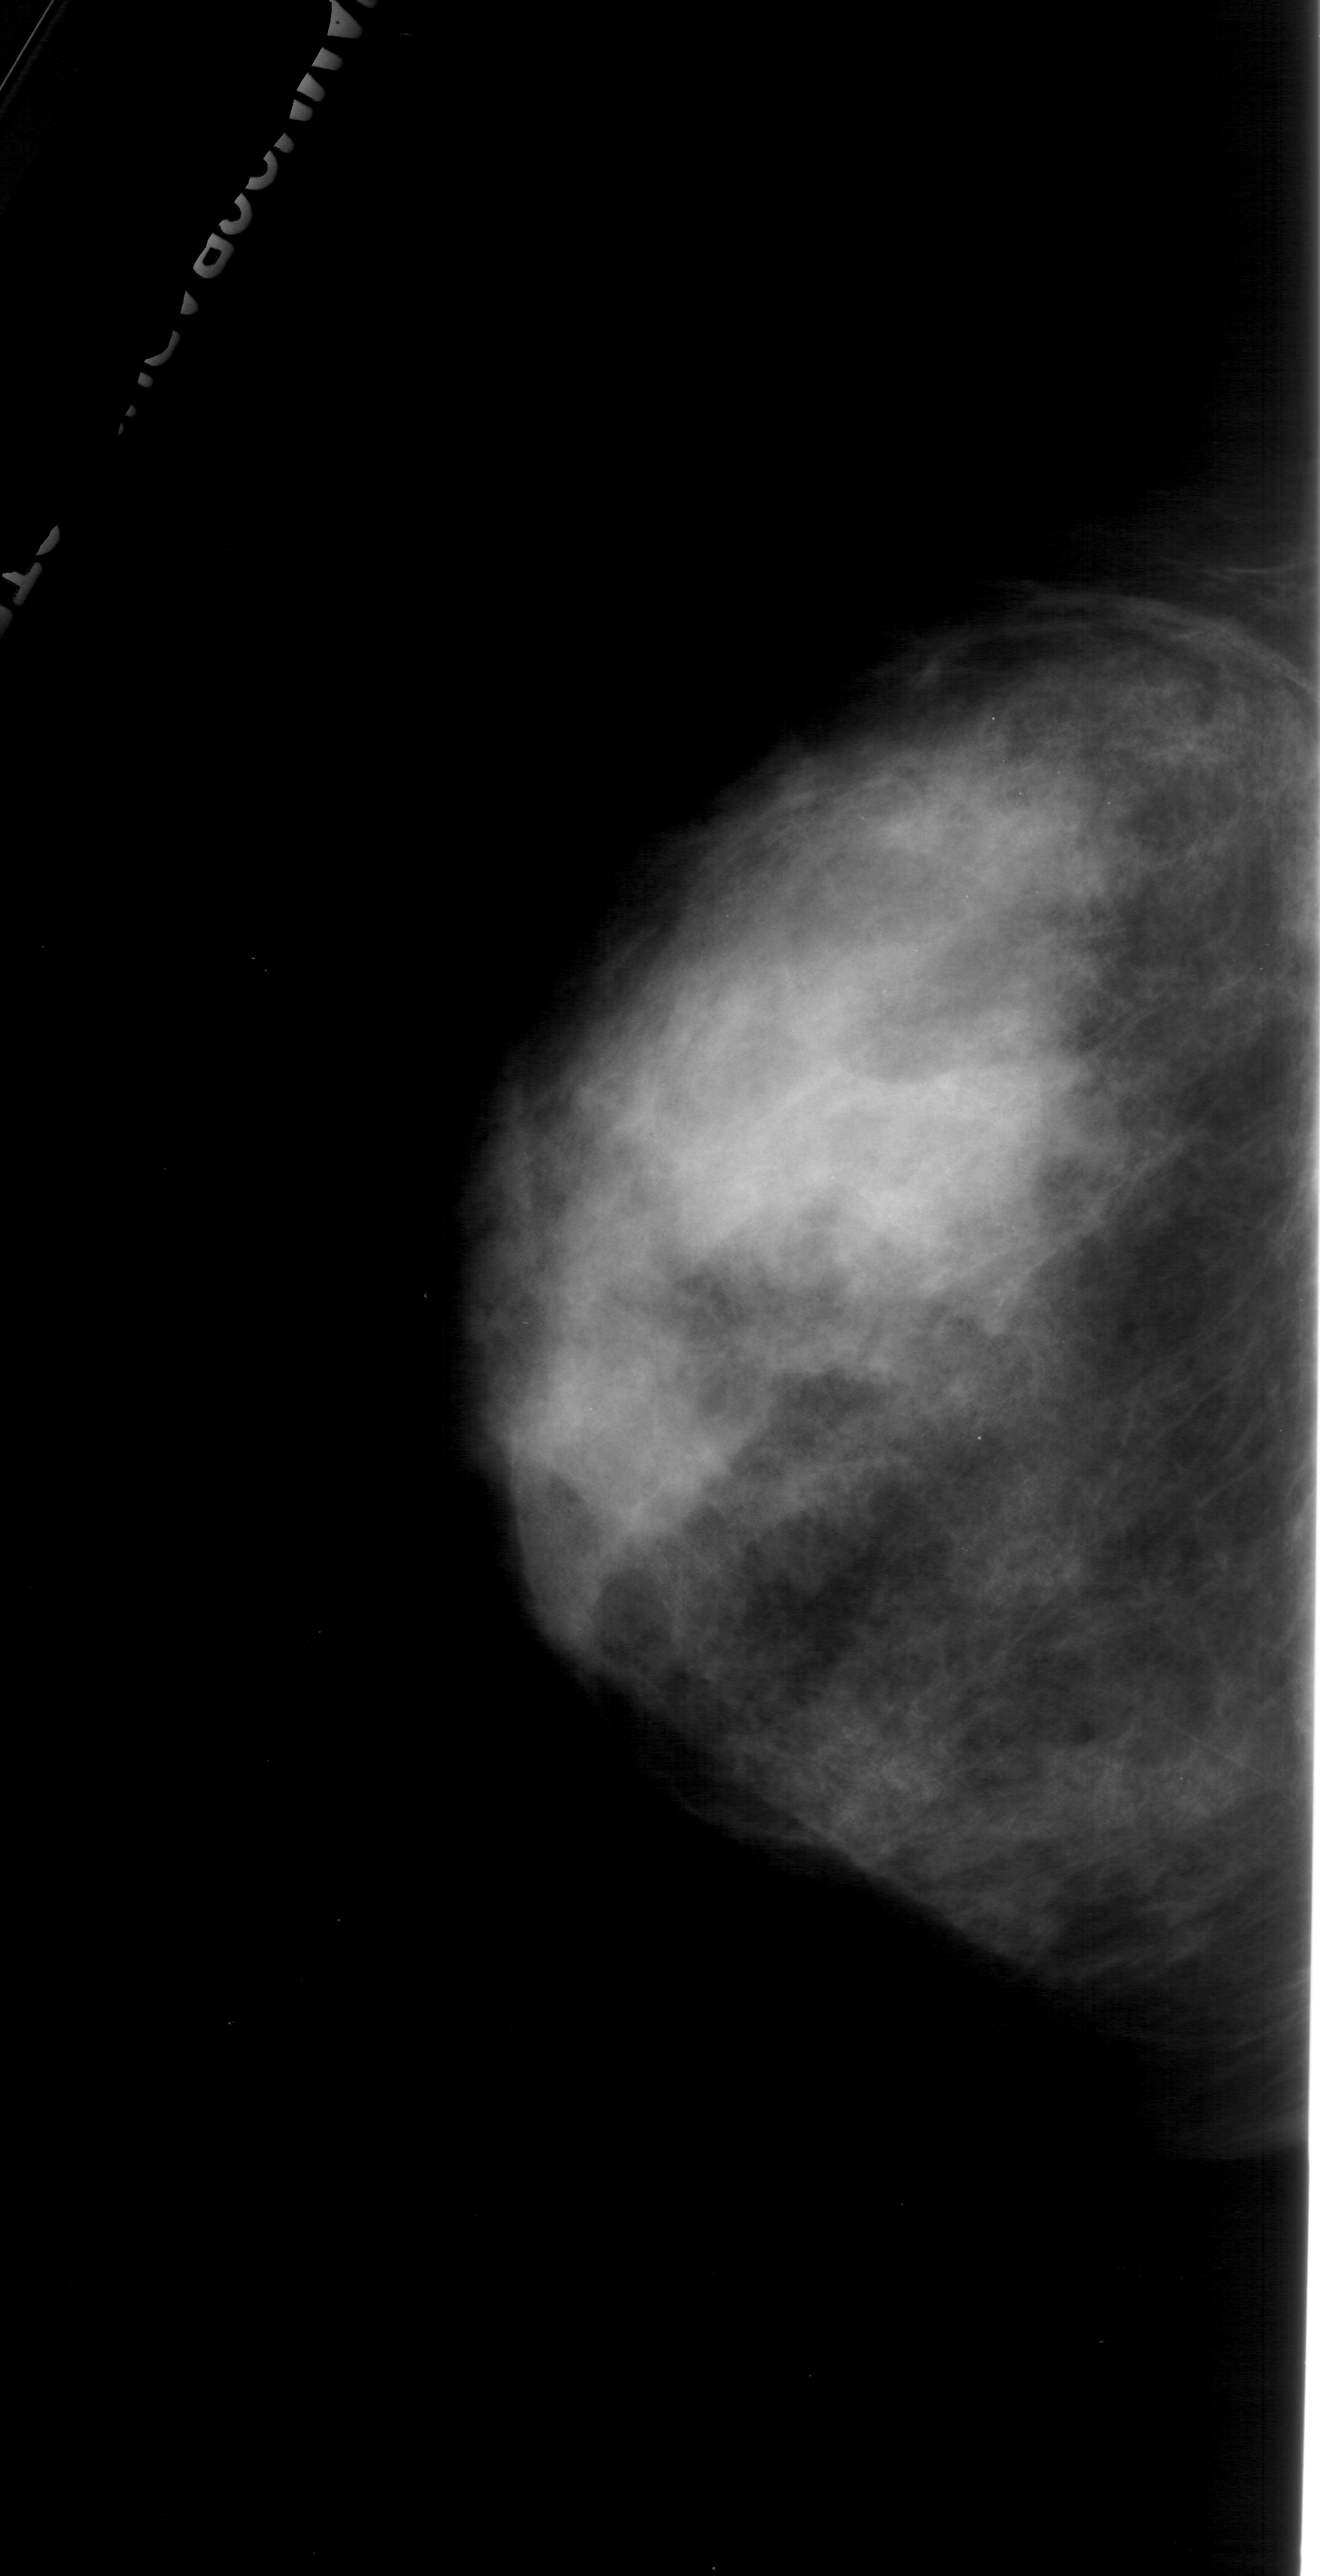
Mammogram (digitized film), left breast, craniocaudal (CC) view, BI-RADS breast density category 4 (scale 1–4).
Calcifications, morphology pleomorphic, distribution segmental; BI-RADS assessment category 4; subtlety rating 1 on a 1 (subtle) to 5 (obvious) scale; pathology result (as recorded, not read from the image): malignant.